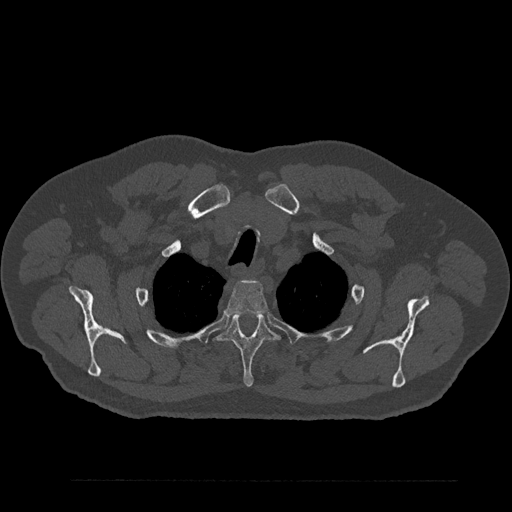
CT including the spine, one axial slice; slice 693 of 797 in the series (ordered by position); bone window (W 1800 / L 400 HU); 0.5 mm slice thickness; 512 × 512 image matrix. Patient: male, 61 years. Case-level facts recorded for this patient, not image findings: primary cancer: prostate.
Annotated regions visible in this slice (semi-automatic segmentation, software-assisted and operator-edited):
- T2 vertebra: bounding box <224,279,268,316> (left, top, right, bottom; pixels)
- T3 vertebra: <218,314,278,387>